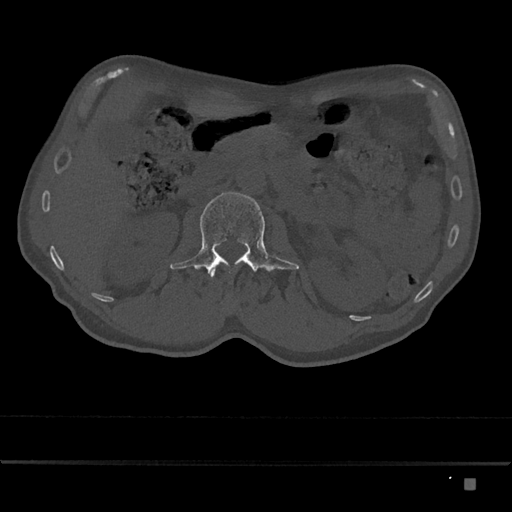
CT including the spine, one axial slice; slice 486 of 797 in the series (ordered by position); 120 kVp; bone window (W 1800 / L 400 HU); 512 × 512 image matrix, field of view 390 × 390 mm. Patient: male, 72 years. Case-level facts recorded for this patient, not image findings: primary cancer: prostate.
Outlined on this slice (semi-automatically segmented with operator editing):
- L1 vertebra: bounding box <210,269,215,278> (left, top, right, bottom; pixels)
- L2 vertebra: <170,192,299,274>